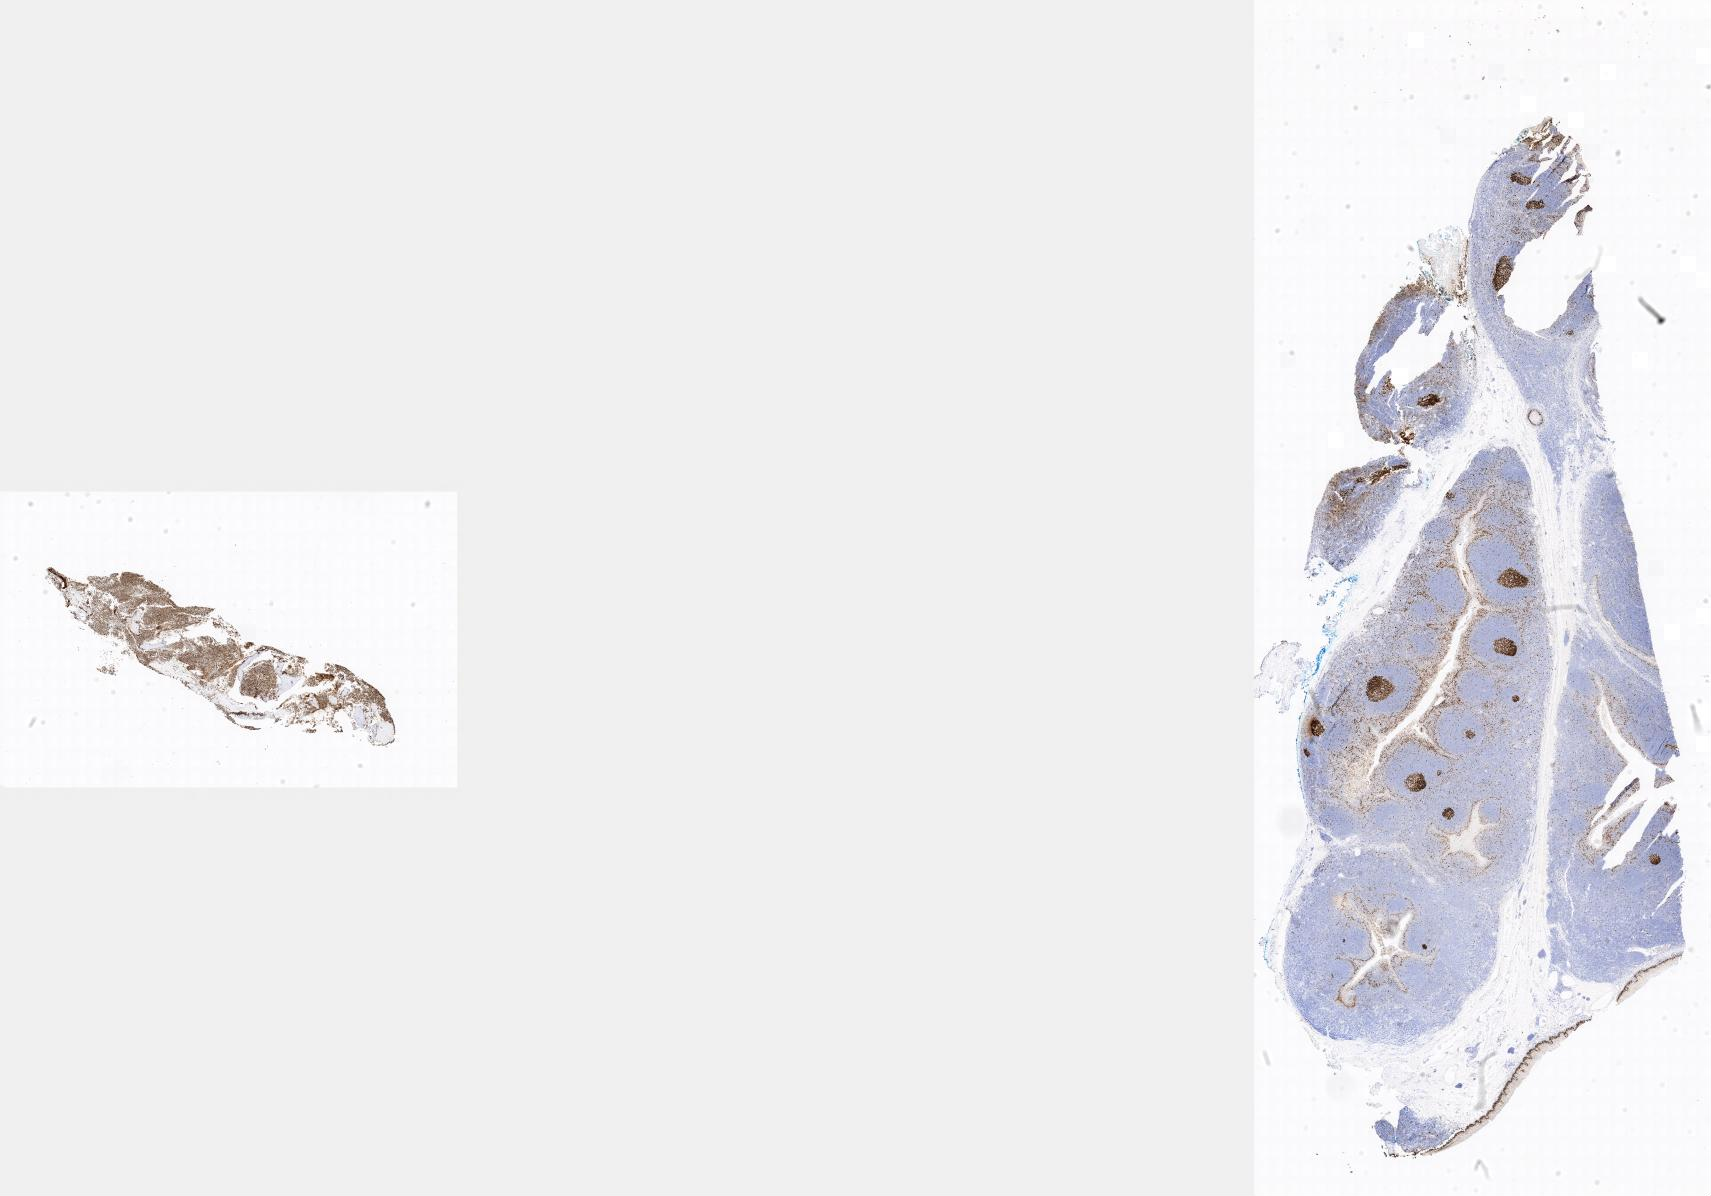
Whole-slide image, immunohistochemical stain for Ki-67 — whole scanned area shown as a low-resolution overview. Specimen: tumor tissue. Anatomic site: bone marrow. Female patient; age at initial diagnosis 3 years.
Diagnosis: Burkitt lymphoma, NOS.